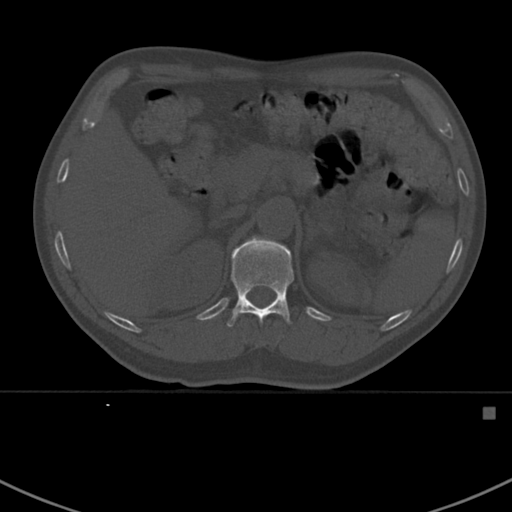
CT including the spine, one axial slice. Position 329 of 412 along the scan axis. Reconstruction kernel Br40s. 120 kVp. Bone window (W 1800 / L 400 HU). 1.5 mm slice thickness. 512 × 512 image matrix. Male patient, age 59 years. From the clinical record (not read from this slice): primary cancer: prostate.
Annotated regions visible in this slice (semi-automatically segmented with operator editing):
- T12 vertebra: bounding box (x1, y1, x2, y2) in pixels: (227, 237, 294, 327)